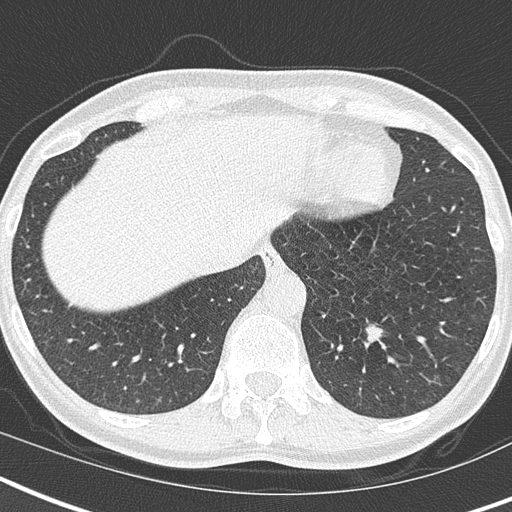
Chest CT (low-dose screening protocol), one axial image, third screening round (two years after baseline), lung window (W 1500 / L -600 HU), lung (sharp) reconstruction kernel (B50f), 120 kVp, slice 128 of 173 in the series. Female participant, aged 55 years at enrolment. Current smoker at enrolment.
Expert-annotated lung lesion, bounding box <349,309,401,360> (left, top, right, bottom; pixels). The screening reader recorded 2 non-calcified nodules or masses ≥4 mm on this exam (left lower lobe, right upper lobe); which of them this box marks is not recorded. Official screen result: positive, other.